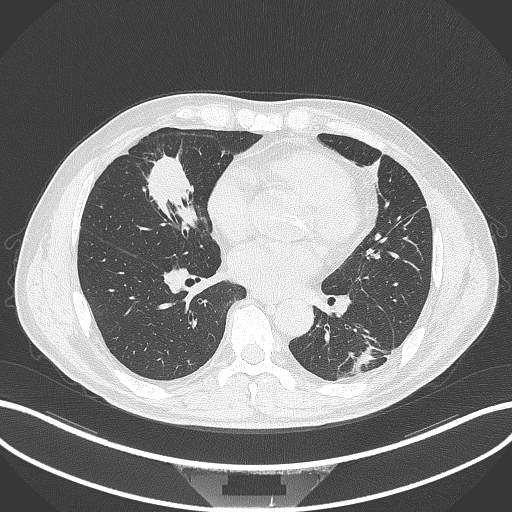
Chest CT, one axial slice; slice 127 of 399 in the series (ordered by position); reconstruction kernel B70f; 120 kVp; lung window (W 1500 / L -600 HU); 1 mm slice thickness; 512 × 512 image matrix. Male patient, age 59 years. Case-level facts recorded for this patient, not image findings: clinical TNM (as recorded): T2a N1 M0.
Outlined on this slice (bounding box drawn by a radiologist):
- lung tumour (recorded histology: adenocarcinoma): bounding box <140,153,206,235> (left, top, right, bottom; pixels)